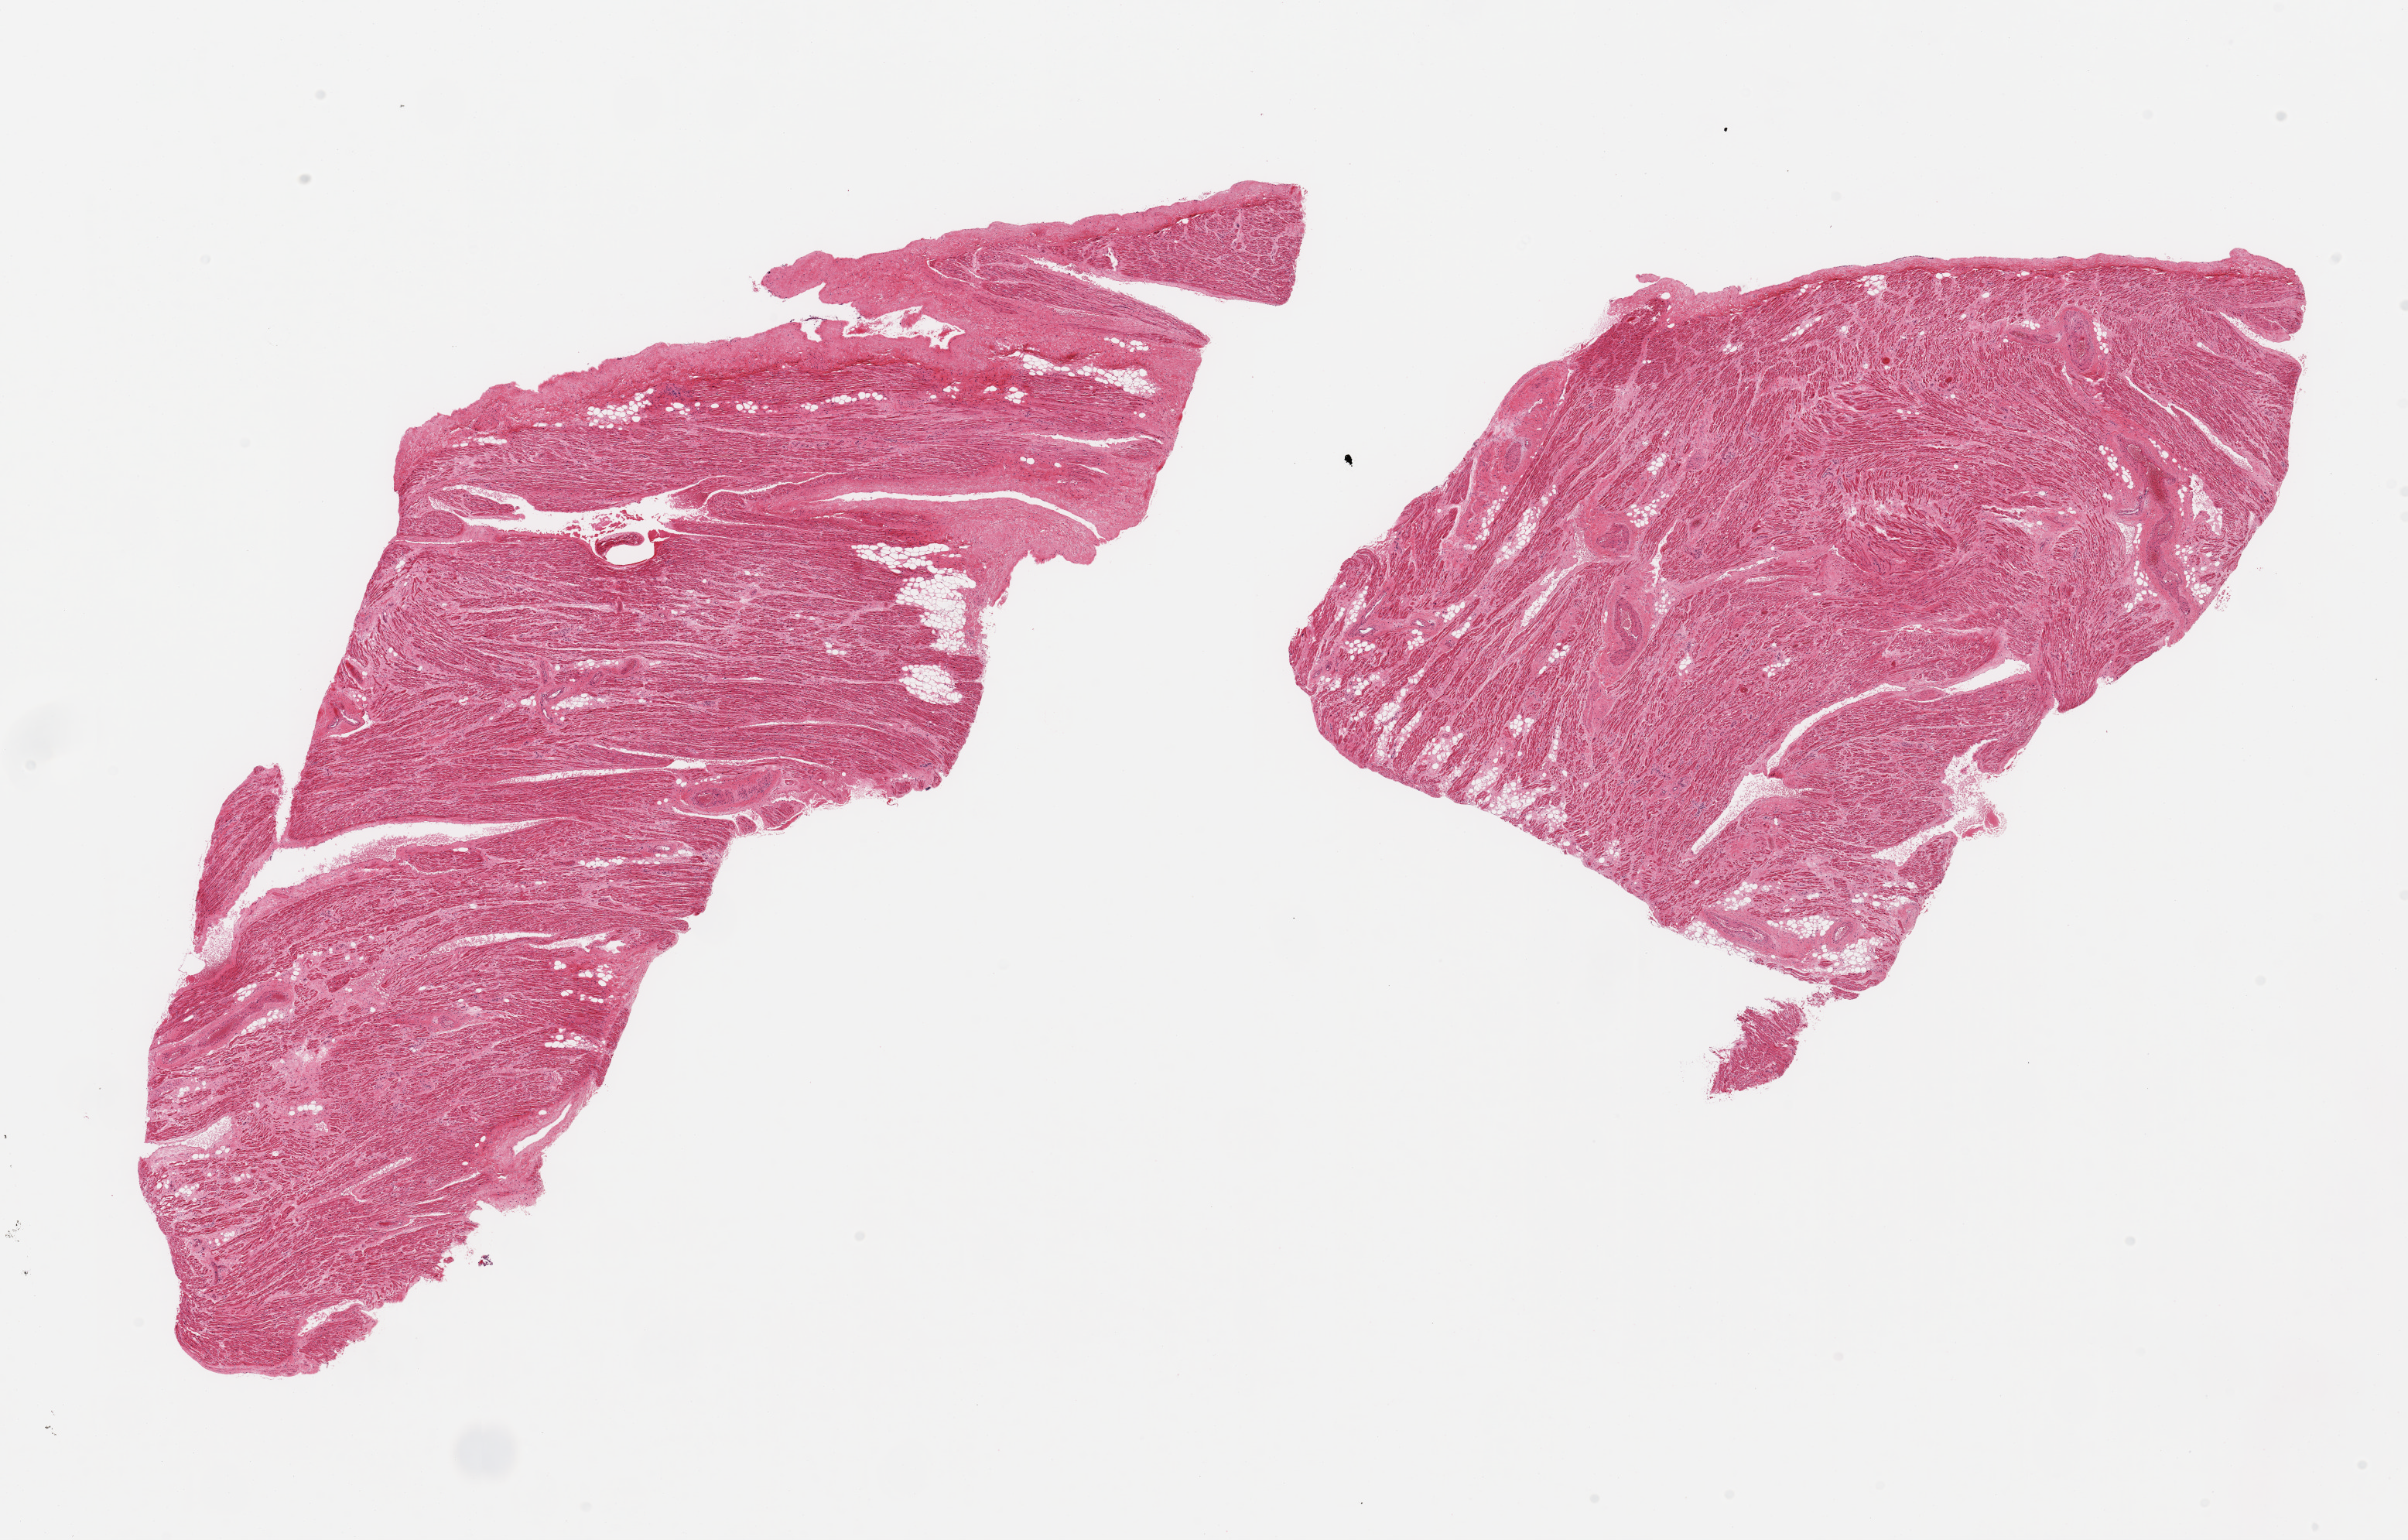
Whole-slide image, H&E stain, shown as a low-resolution overview of the whole scanned area (about 24.6 x 15.7 mm), PAXgene-fixed paraffin-embedded (PFPE) section, section of auricular appendage (target tissue), donor tissue sample. Donor sex: male.
Pathologist's review note for this sample: 2 pieces, no abnormalities.